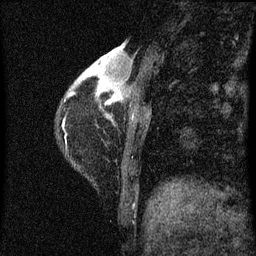
Breast MRI (dynamic contrast-enhanced), one sagittal slice. Slice 13 of 60 in the series (ordered by position). Dynamic contrast-enhanced series, image 2 of 3 at this slice position (ordered by acquisition). 1.5 T. TE 4.2 ms, TR 8 ms. 256 × 256 image matrix, field of view 180 × 180 mm. Patient: female, 38 years.
Structures marked on this image (semi-automatic segmentation, software-assisted and operator-edited):
- analysis volume of interest (the breast-tissue region the enhancement analysis was run in; not a lesion): bounding box (x1, y1, x2, y2) in pixels: (67, 42, 144, 127)
- tumour enhancement mask (voxels above the 70 % enhancement threshold inside the analysis volume of interest): (68, 62, 122, 103)